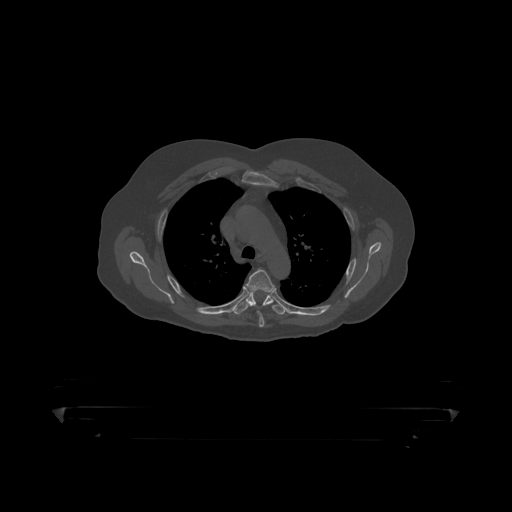
CT including the spine, one axial slice; slice 330 of 390 in the series (ordered by position); reconstruction kernel STANDARD; 120 kVp; bone window (W 1800 / L 400 HU); 1.25 mm slice thickness; 512 × 512 image matrix. Male patient, age 60 years. From the clinical record (not read from this slice): primary cancer: prostate.
Annotated regions visible in this slice (semi-automatically segmented with operator editing):
- T4 vertebra: bounding box (x1, y1, x2, y2) in pixels: (247, 270, 276, 319)
- T5 vertebra: (233, 292, 287, 315)